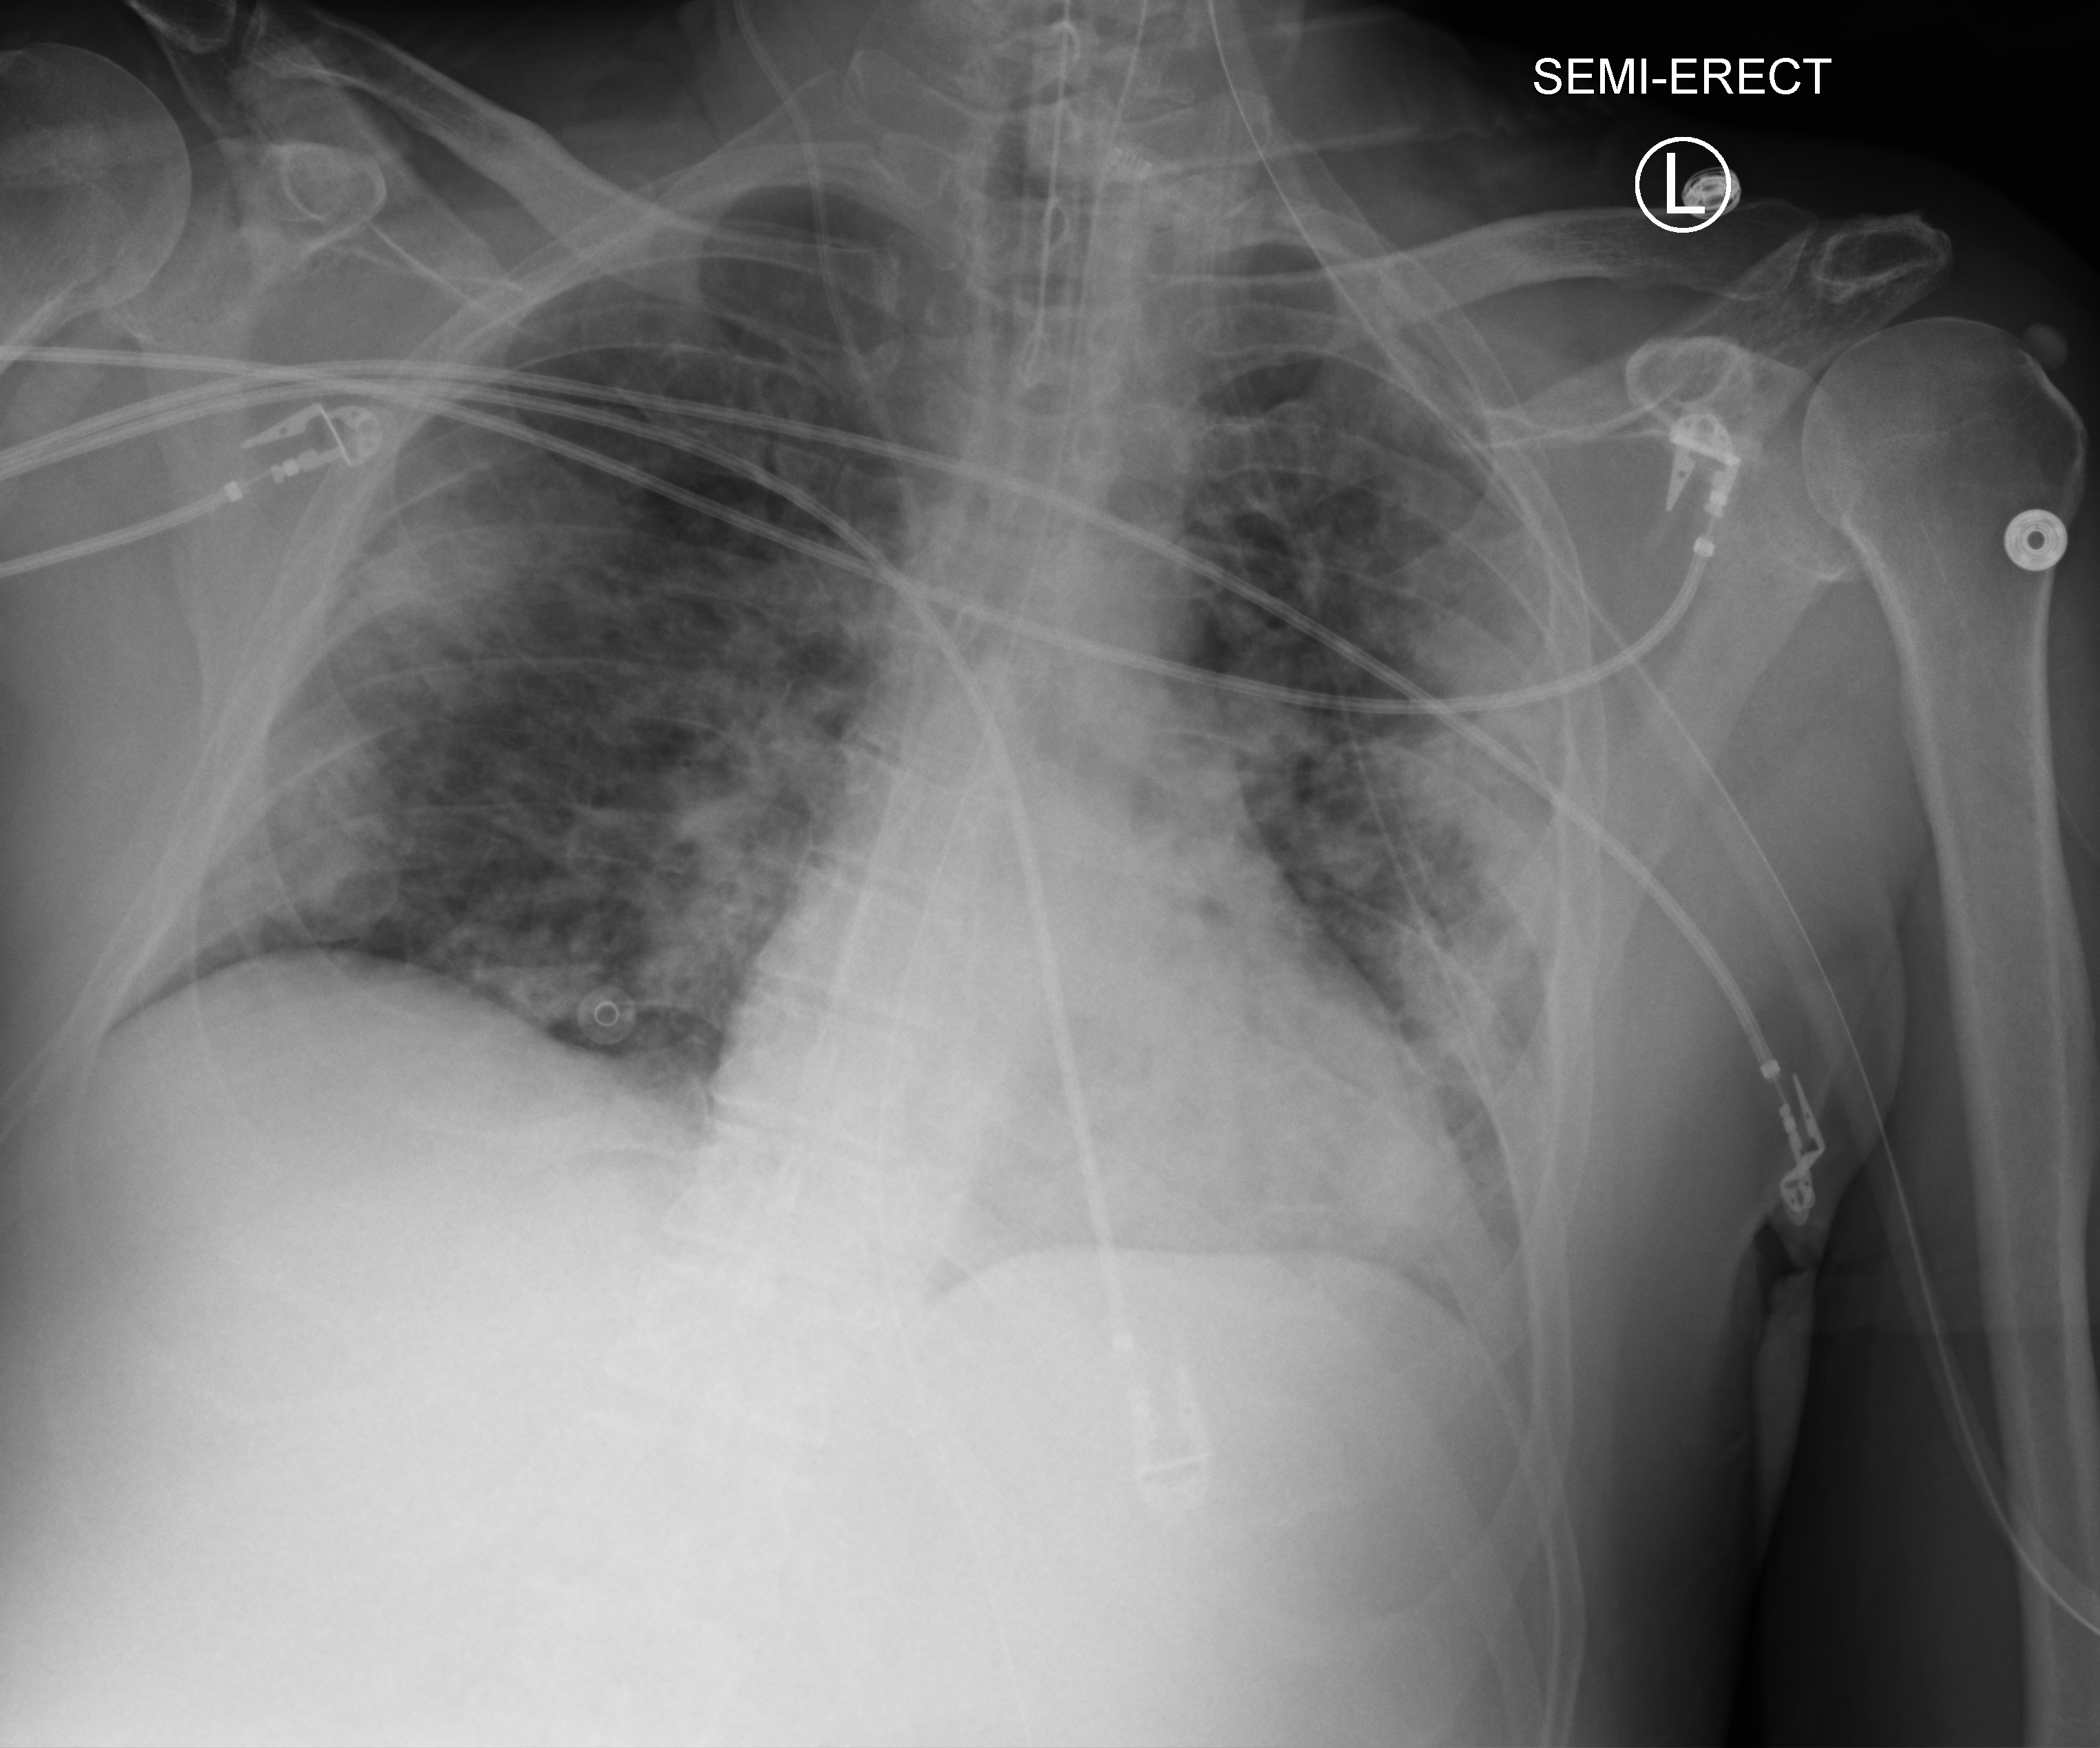
Chest X-ray (portable). Male patient hospitalised with COVID-19, age 18–59 years.
From the hospital-stay record, not from the radiograph (when in the stay this image was taken is not recorded): COPD (admission record): no.